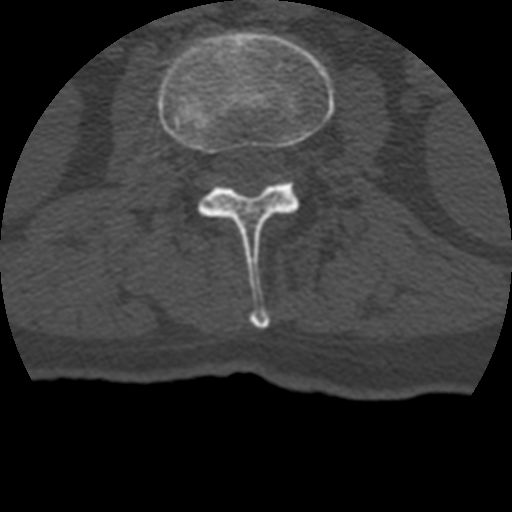
CT including the spine, one axial slice. Position 112 of 399 along the scan axis. Bone window (W 1800 / L 400 HU). 1.25 mm slice thickness. 512 × 512 image matrix. Patient age 69 years. Case-level facts recorded for this patient, not image findings: primary cancer: prostate.
Annotated regions visible in this slice (semi-automatic segmentation, software-assisted and operator-edited):
- L2 vertebra: bounding box <158,31,335,329> (left, top, right, bottom; pixels)